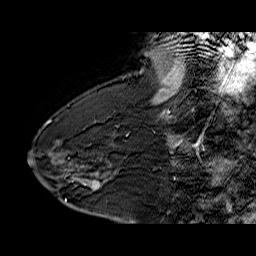
Breast MRI (dynamic contrast-enhanced), one sagittal slice. Position 41 of 60 along the scan axis. Dynamic contrast-enhanced series, time point 2 of 6 at this slice position (early post-contrast). 1.5 T. TE 6.4 ms, TR 32.9 ms. 256 × 256 image matrix. Female patient. Case-level facts recorded for this patient, not image findings: setting: breast cancer imaged before/during neoadjuvant chemotherapy; receptor status: HR-positive, HER2-negative.
Structures marked on this image (semi-automatically segmented with operator editing):
- analysis volume of interest (the breast-tissue region the enhancement analysis was run in; not a lesion): bounding box (x1, y1, x2, y2) in pixels: (68, 155, 126, 203)
- tumour enhancement mask (voxels above the 100 % enhancement threshold inside the analysis volume of interest): (91, 181, 98, 189)